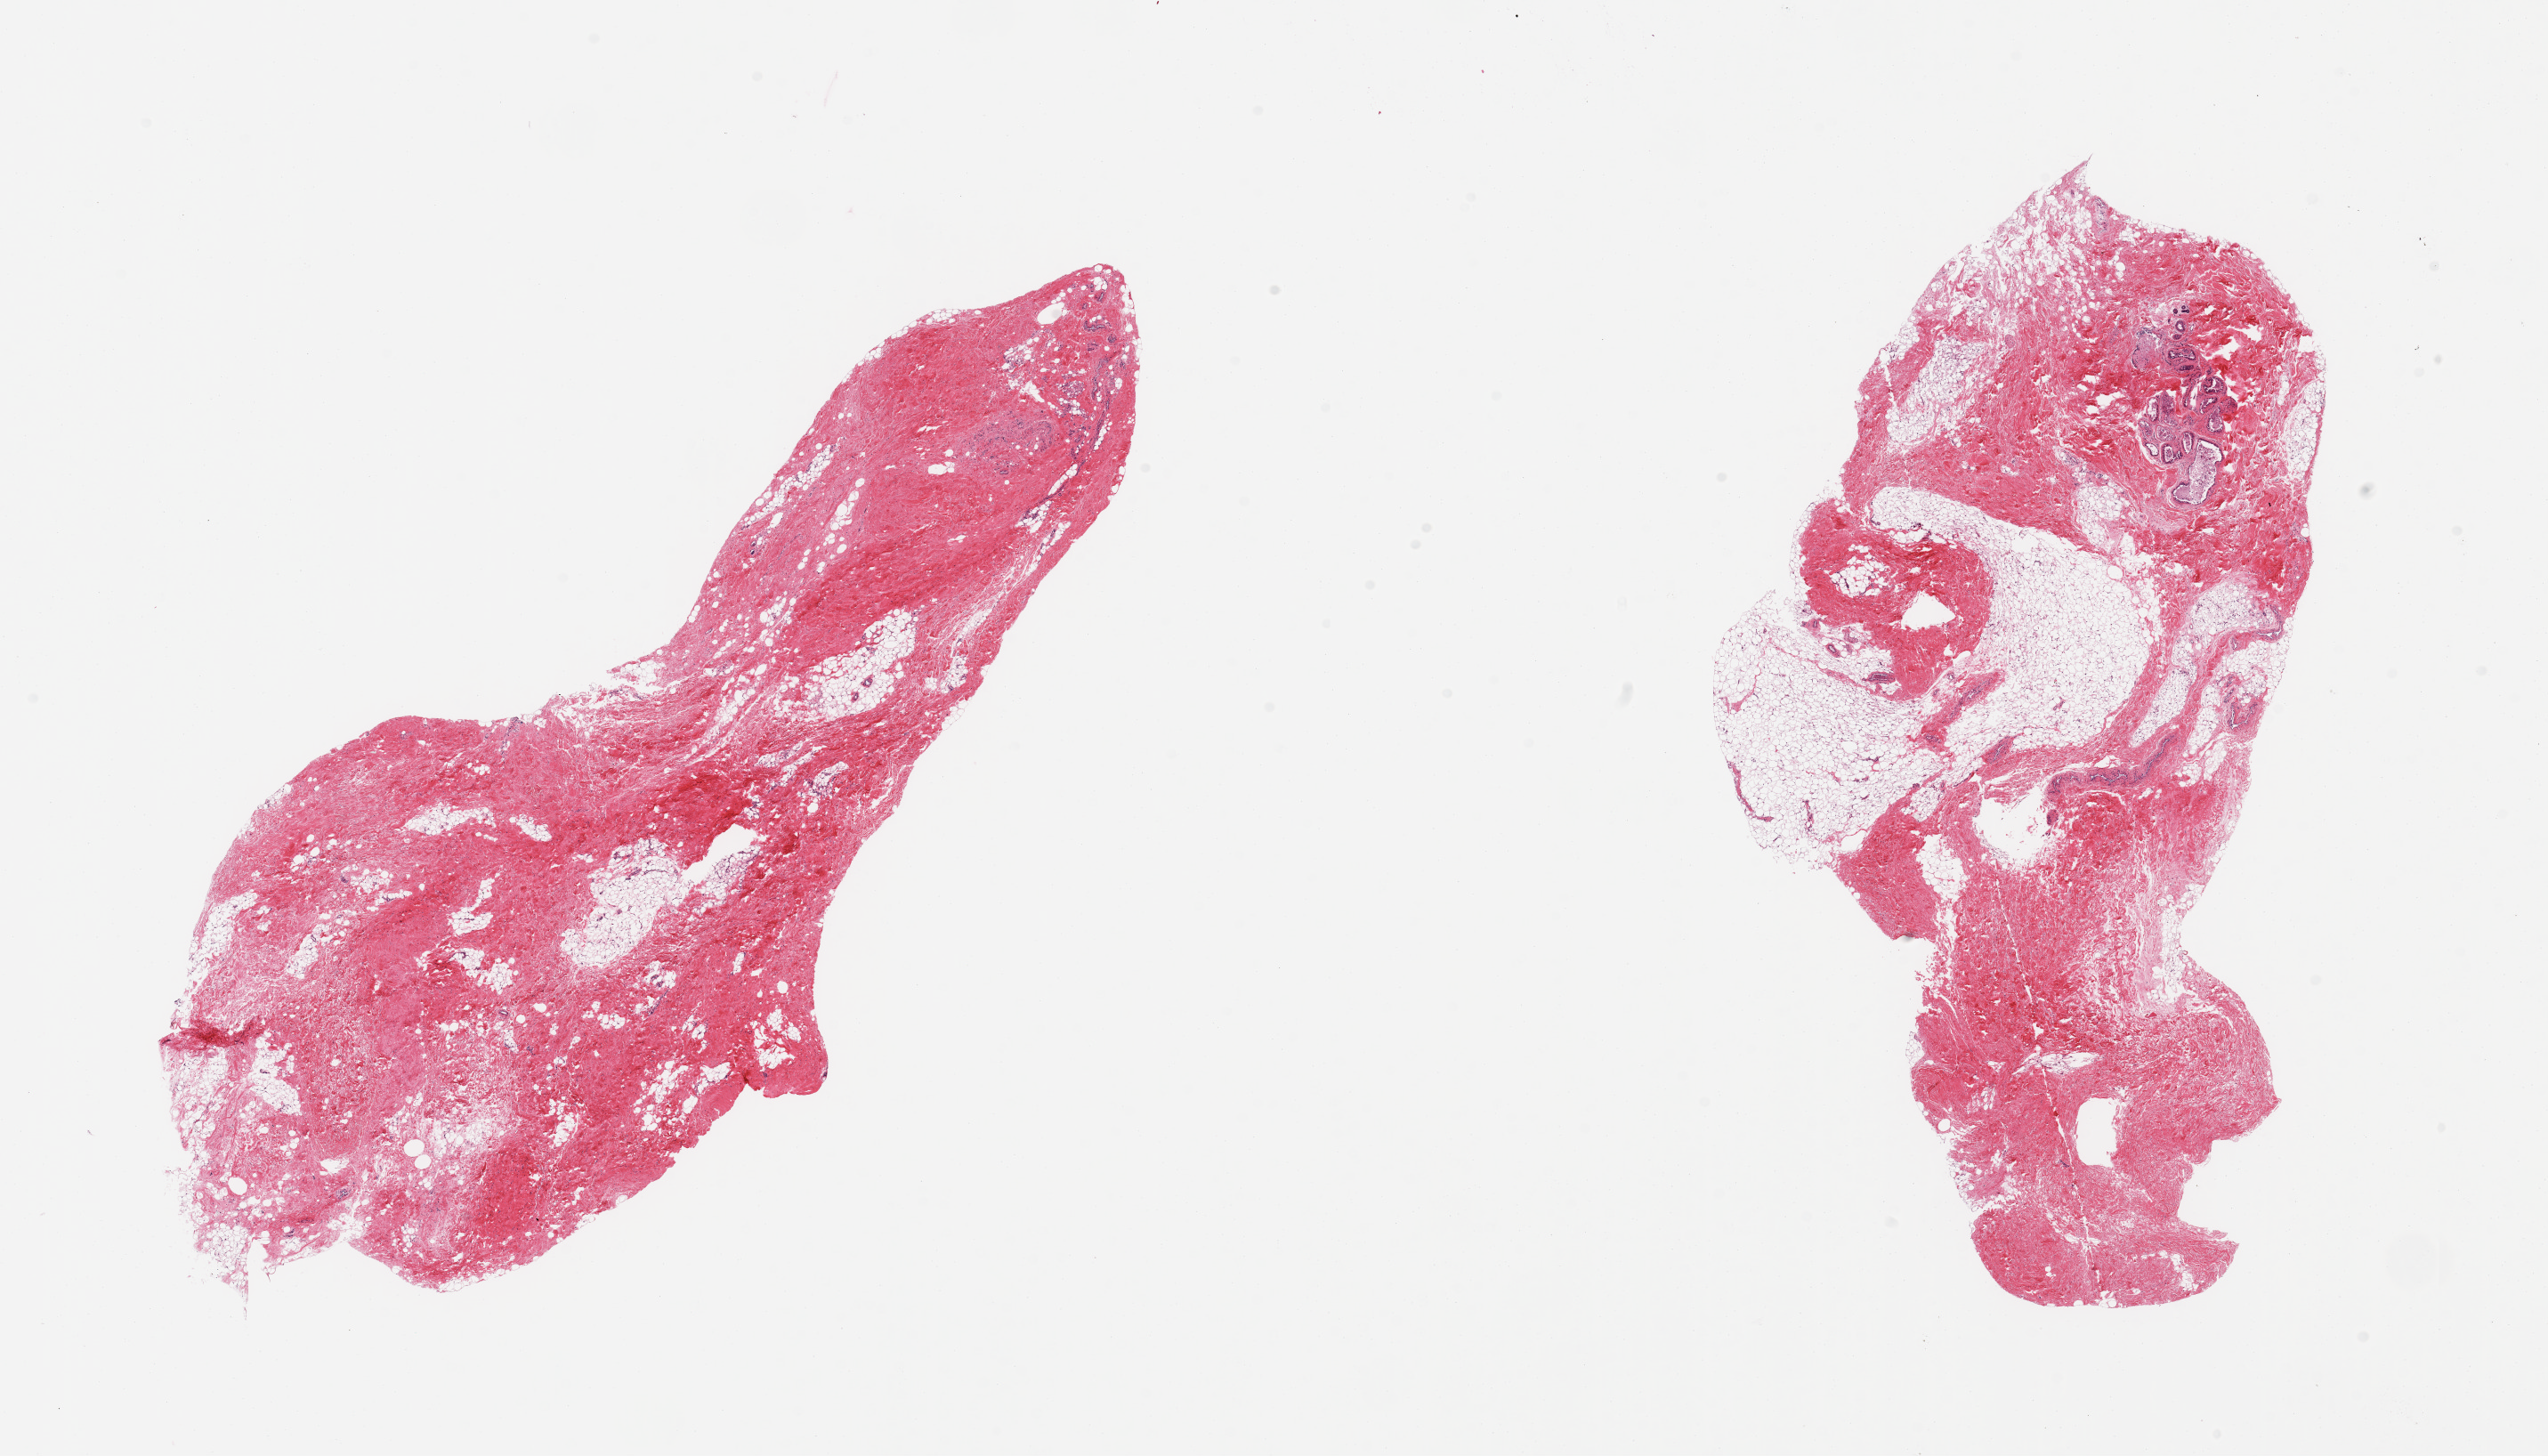
Whole-slide image, hematoxylin and eosin (H&E) stain — shown as a low-resolution overview of the whole scanned area (about 22.6 x 12.9 mm), PAXgene-fixed paraffin-embedded (PFPE) section, sampled site (target tissue): breast, tissue donor sample. Male donor.
Review note (as recorded): 2 pieces; 20-30% fat, remainder is dense stroma with focus of ductal epithelium with apocrine and cystic change.